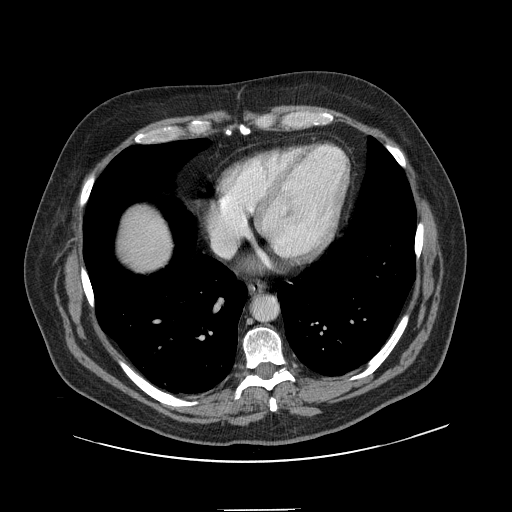
Contrast-enhanced abdominal CT, one axial slice; slice 144 of 154 in the series (ordered by position); intravenous contrast given; soft-tissue window (W 400 / L 40 HU); 2.5 mm slice thickness; 512 × 512 image matrix. Male patient, age 61 years. Case-level facts recorded for this patient, not image findings: diagnosis: colorectal cancer liver metastases, imaged before liver resection; multiple liver metastases: yes; largest metastasis: 2.6 cm; chemotherapy before resection: no.
Outlined on this slice (outlined manually by an expert reader):
- liver: bounding box <122,206,170,270> (left, top, right, bottom; pixels)
- planned liver remnant (the part of the liver to remain after resection): <123,206,170,271>